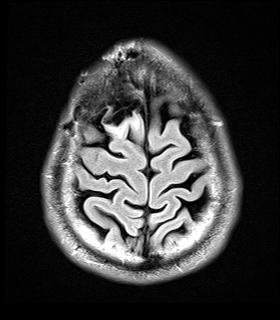
Brain MRI from a brain-tumour surgery series, one axial slice; position 5 of 32 along the scan axis; T2 FLAIR; 280 × 320 image matrix, field of view 184 × 210 mm. Case-level facts recorded for this patient, not image findings: histopathology: Glial fibroma.
Outlined on this slice (outlined manually by an expert reader):
- tumour: box from (x=105, y=118) to (x=139, y=136) px